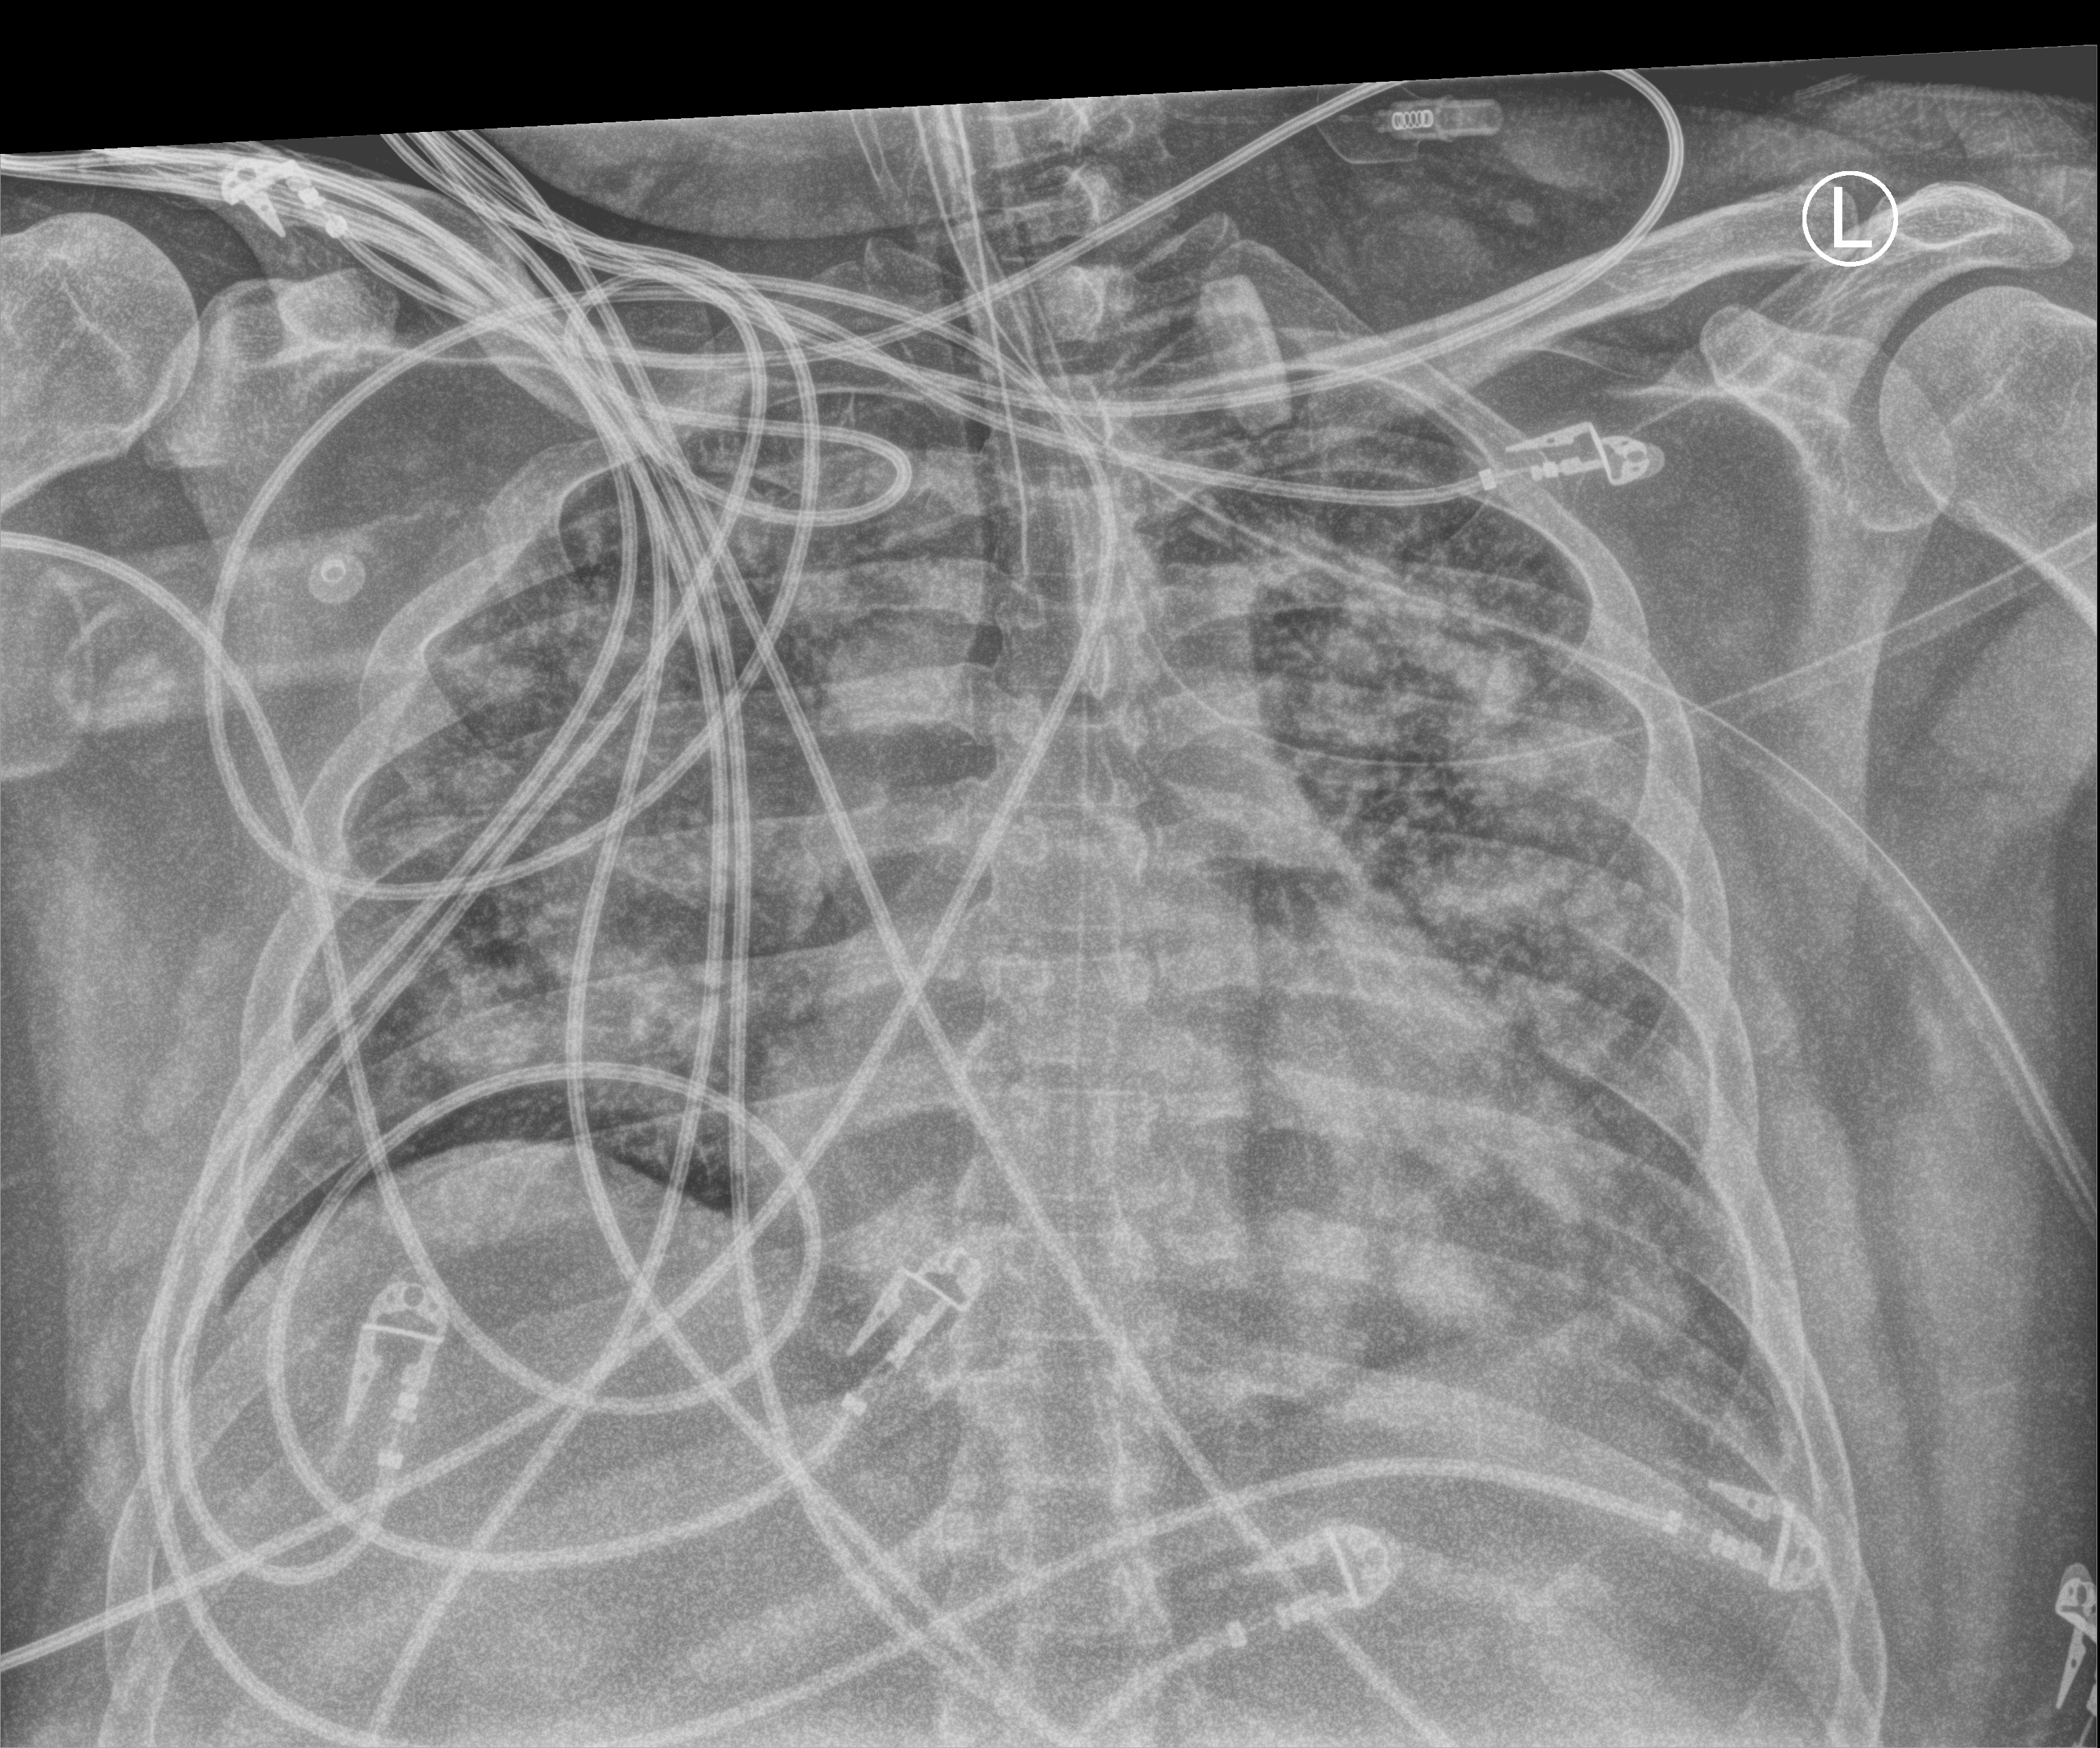
Chest X-ray (portable). Patient hospitalised with COVID-19, aged 18–59 years.
Hospital-stay facts (about this admission, not read from this image; timing relative to this image not recorded): admitted to intensive care during this hospital stay: yes; COPD (admission record): no.